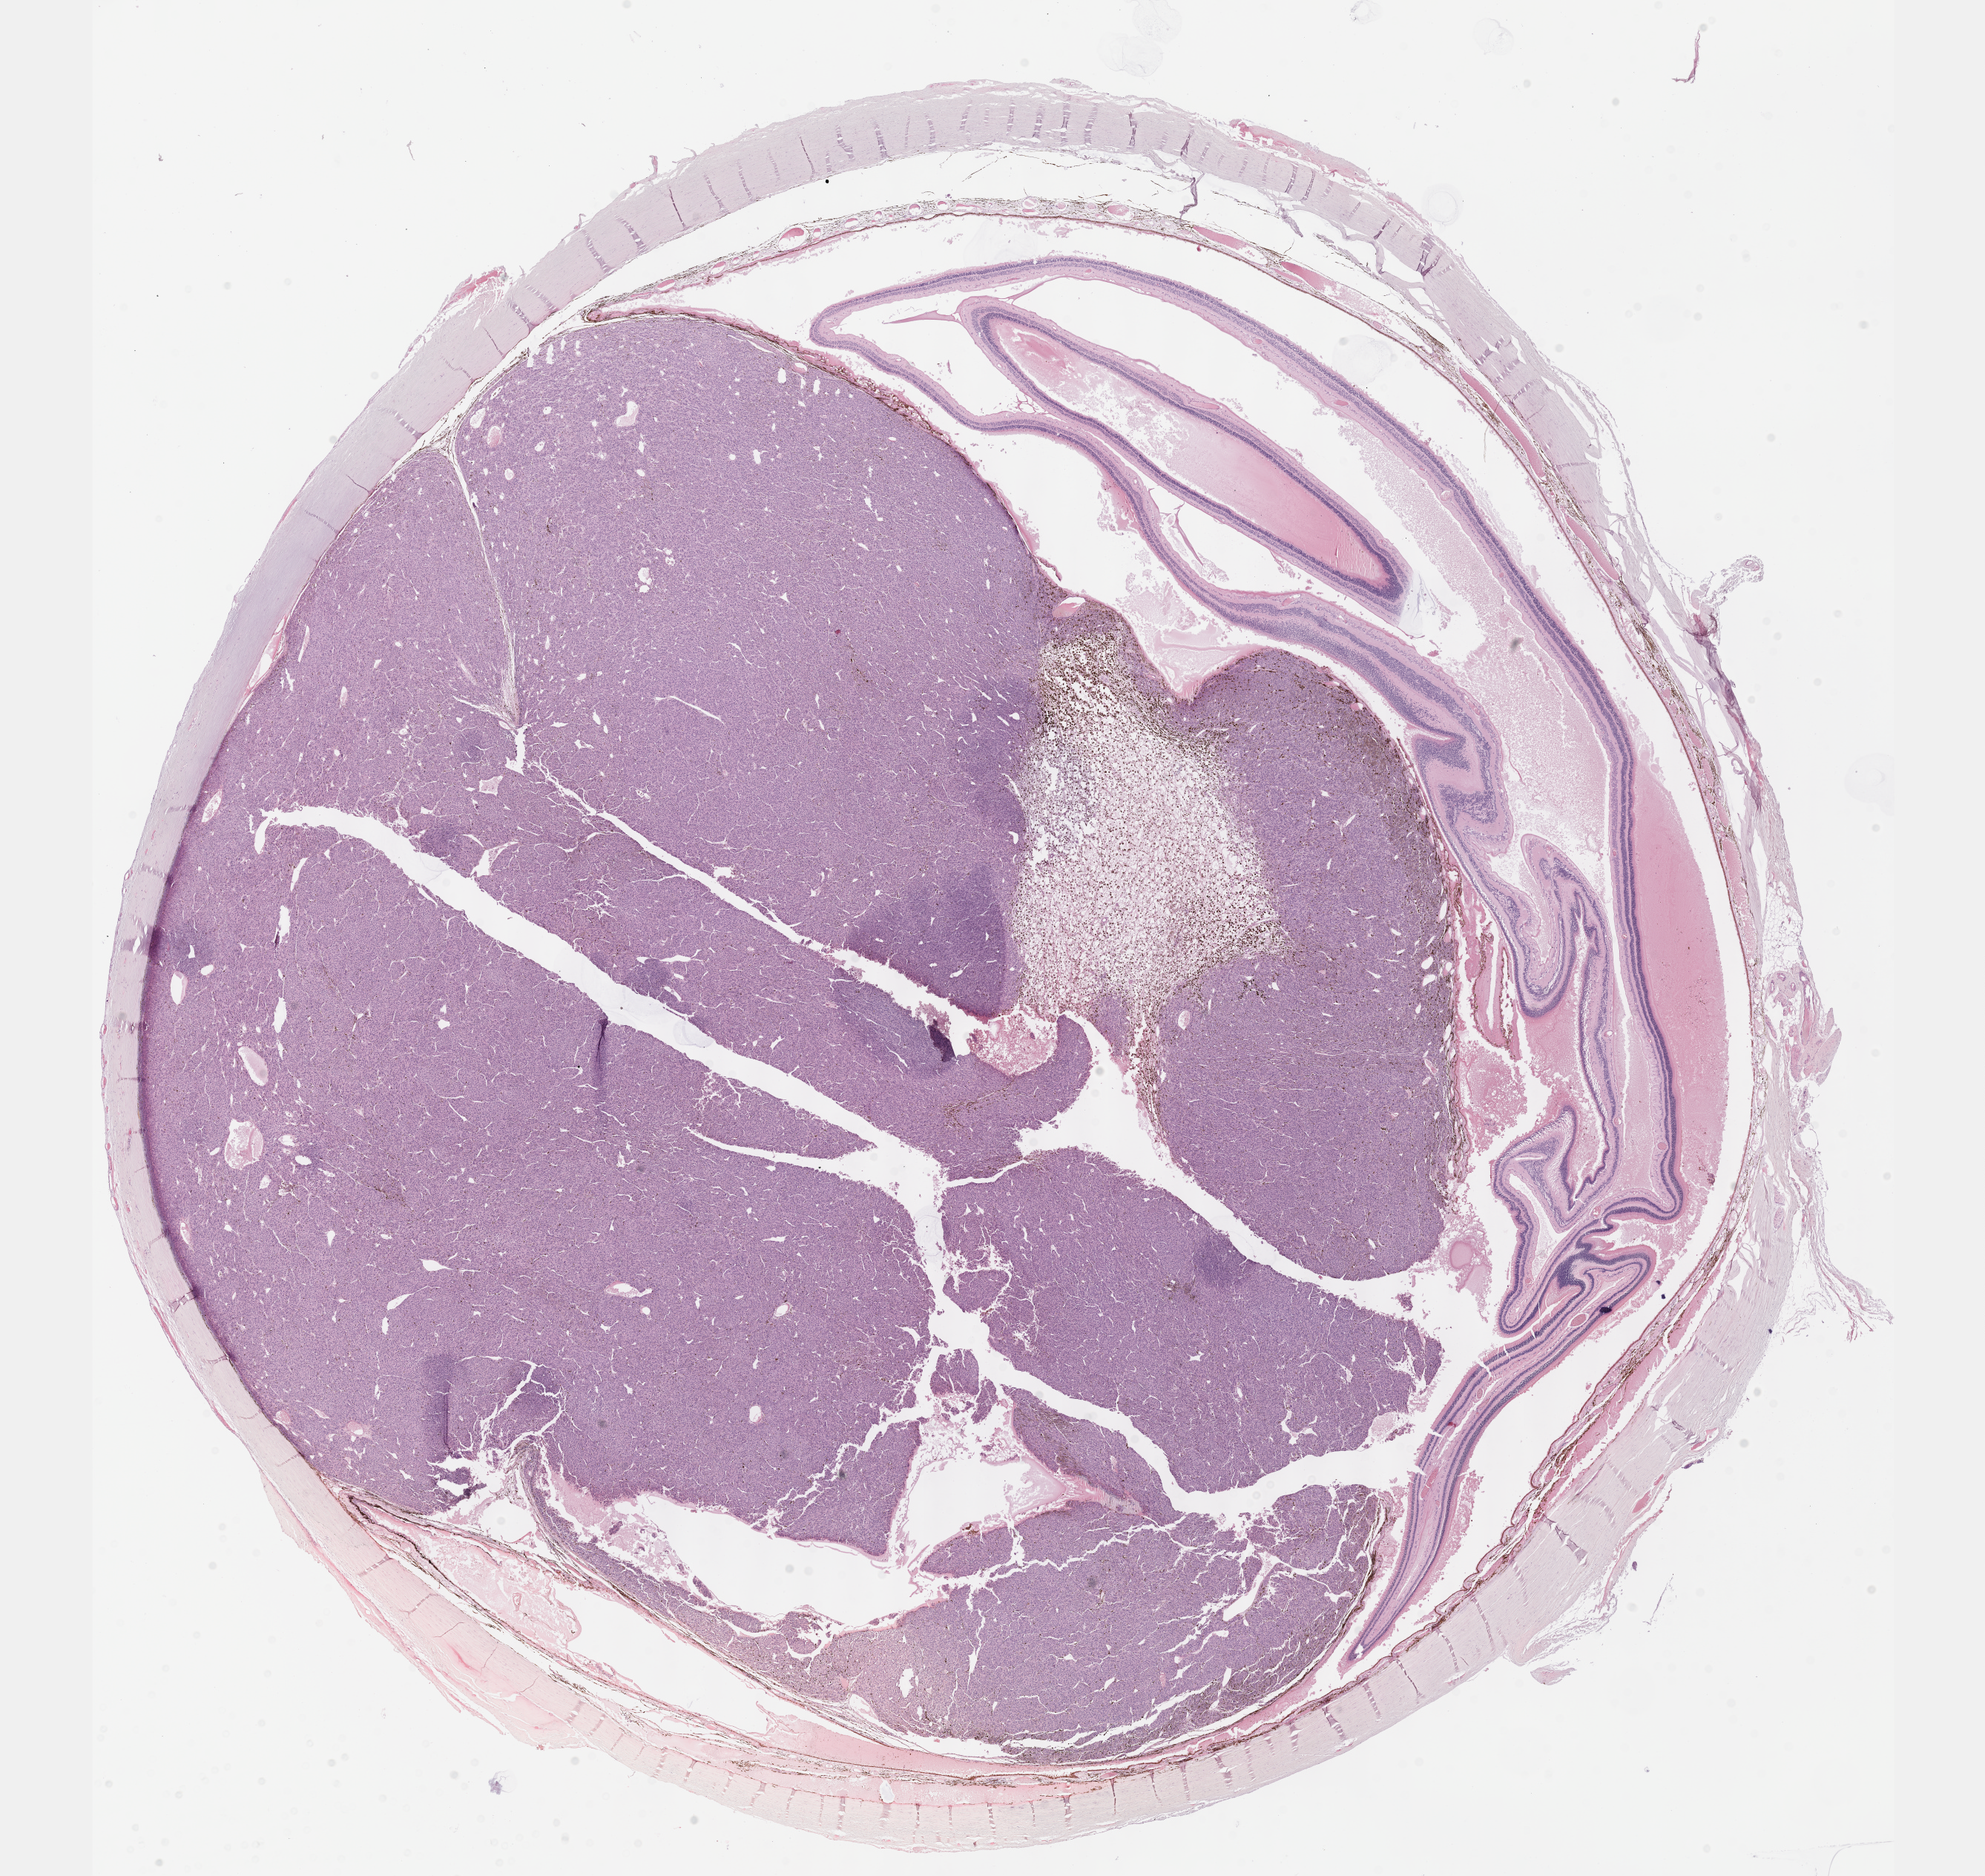
Digitized H&E-stained tissue section (whole slide) — whole scanned area (about 21.6 x 20.4 mm) shown as a low-resolution overview, formalin-fixed paraffin-embedded (FFPE) diagnostic section, sample: primary tumour, uvea. Male, age 74 years at initial diagnosis.
TNM: T4a N0 M0. Pathologic diagnosis: Mixed epithelioid and spindle cell melanoma (ciliary body). AJCC pathologic stage: IIIA (7th edition).